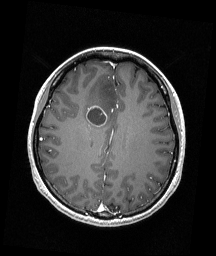
Brain MRI from a brain-tumour surgery series, one axial slice; slice 71 of 192 in the series (ordered by position); T1-weighted post-contrast; 216 × 256 image matrix, field of view 211 × 250 mm. From the clinical record (not read from this slice): histopathology: Astrocytoma; WHO grade: 4; IDH mutation: yes.
Annotated regions visible in this slice (outlined manually by an expert reader):
- tumour: box from (x=85, y=105) to (x=107, y=127) px